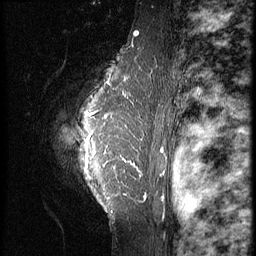
Breast MRI (dynamic contrast-enhanced), one sagittal slice; position 51 of 64 along the scan axis; 3 images stored at this slice position (order not interpretable as contrast timing); 1.5 T; TE 4.2 ms, TR 9 ms; 2.5 mm slice thickness; 256 × 256 image matrix. Patient: female, 39 years. From the clinical record (not read from this slice): setting: breast cancer imaged before/during neoadjuvant chemotherapy; receptor status: HER2-positive.
Outlined on this slice (semi-automatically segmented with operator editing):
- analysis volume of interest (the breast-tissue region the enhancement analysis was run in; not a lesion): bounding box [x1, y1, x2, y2] px = [45, 47, 149, 239]
- tumour enhancement mask (voxels above the 140 % enhancement threshold inside the analysis volume of interest): [85, 79, 145, 197]